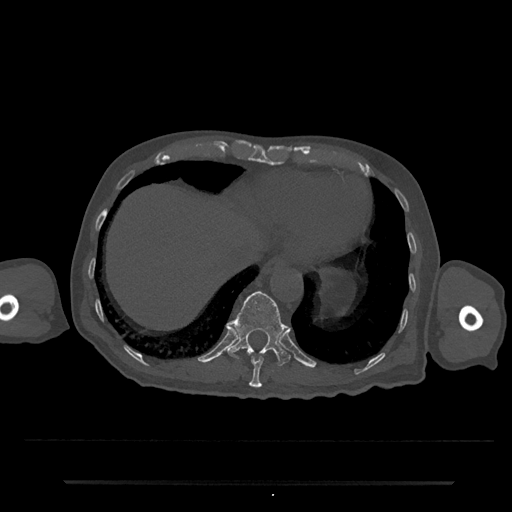
CT including the spine, one axial slice. Slice 274 of 797 in the series (ordered by position). Reconstruction kernel Br40s/3. 120 kVp. Bone window (W 1800 / L 400 HU). 0.5 mm slice thickness. 512 × 512 image matrix. Male patient, age 74 years. From the clinical record (not read from this slice): primary cancer: prostate.
Outlined on this slice (semi-automatically segmented with operator editing):
- T10 vertebra: bounding box <249,356,264,388> (left, top, right, bottom; pixels)
- T11 vertebra: <227,291,291,366>